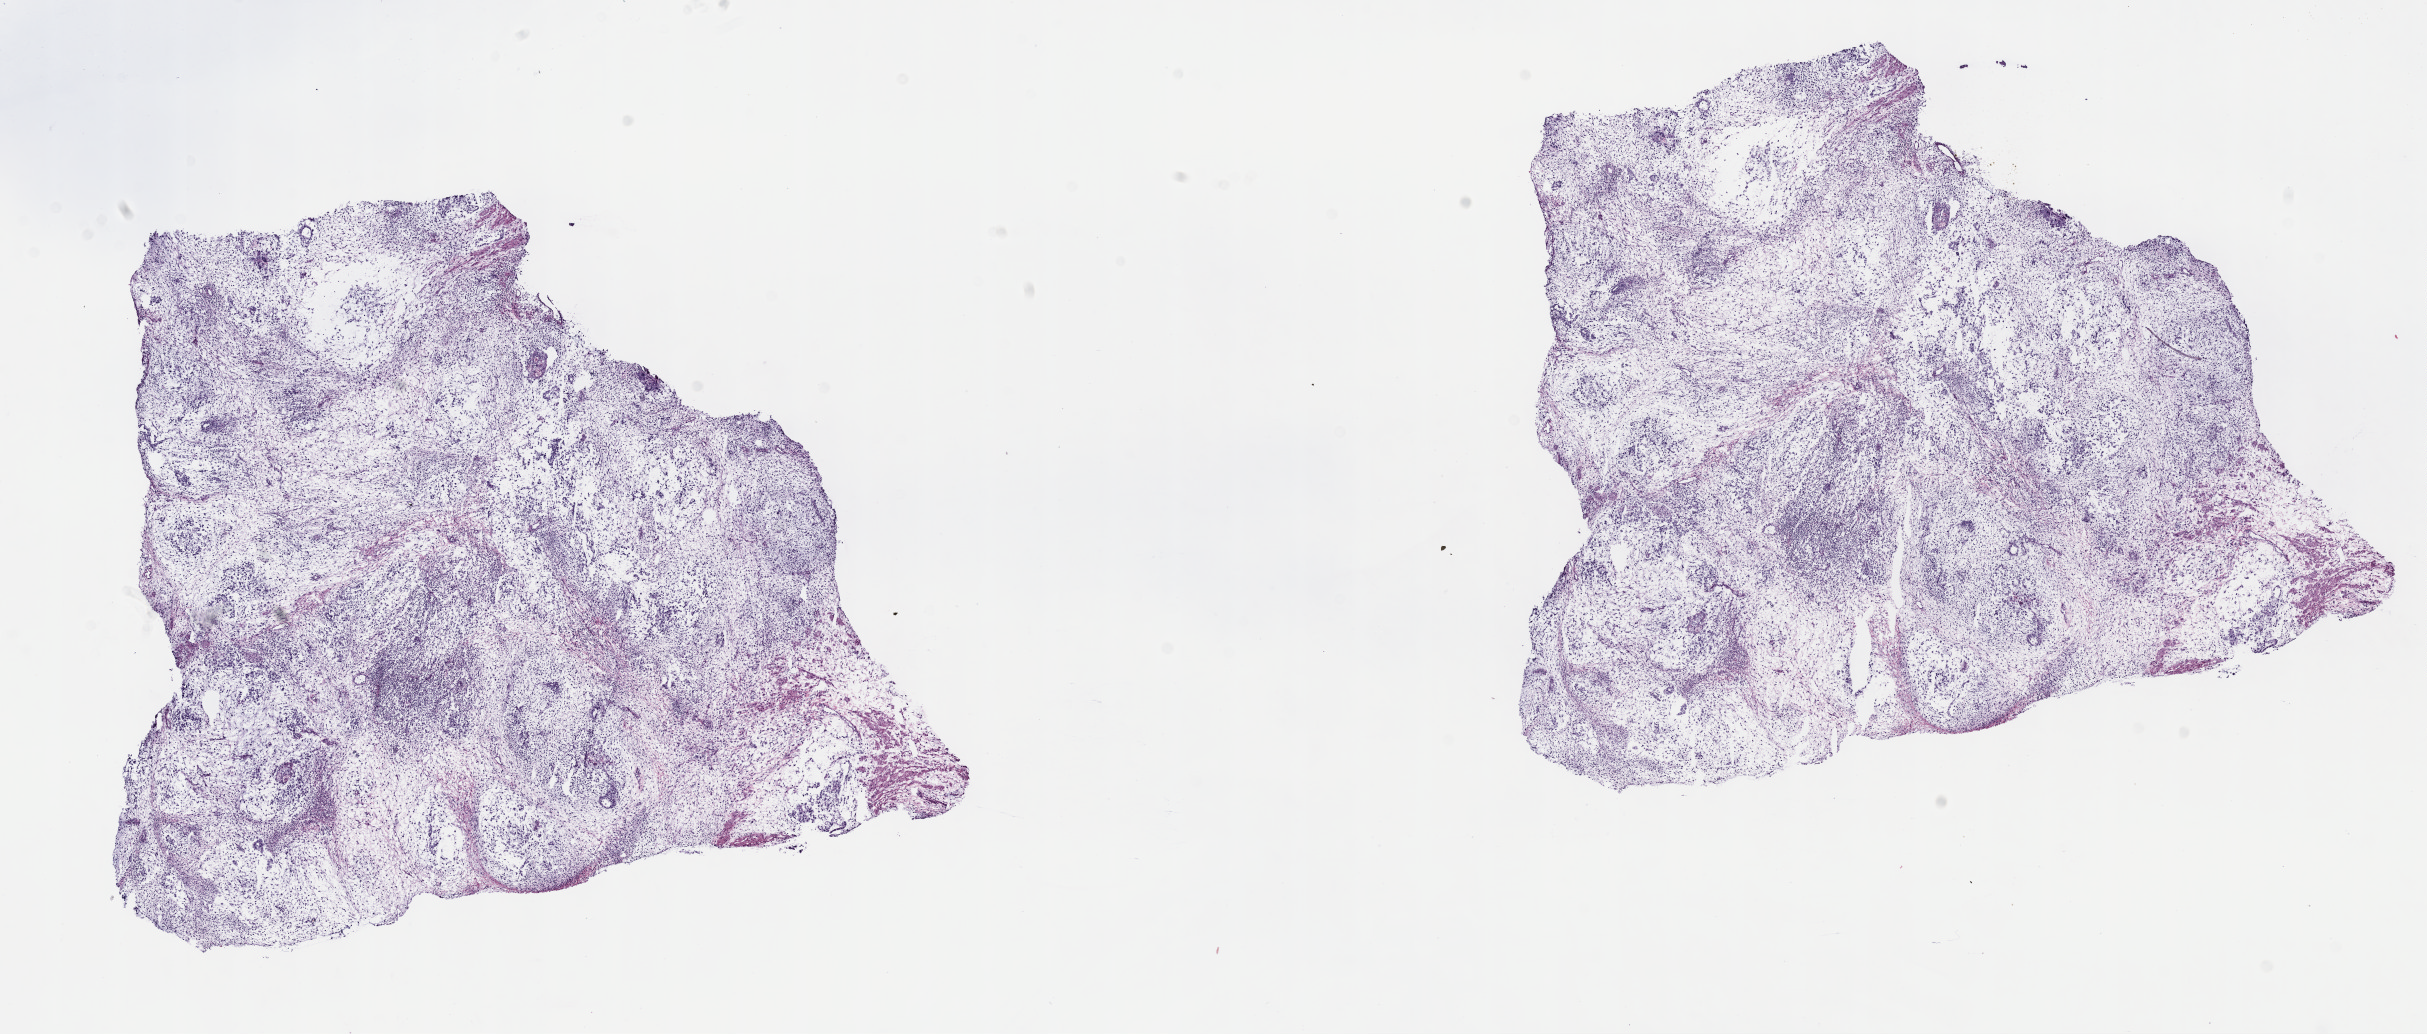
Digitized H&E tissue section (whole slide) — whole scanned area (about 19.6 x 8.4 mm, slide scanned at 40x) shown as a low-resolution overview, frozen section from the top of the tissue portion, primary tumour sample from the testis. Male, age 20 years at initial diagnosis. Composition of this section per pathologist review: tumour cells 100%, tumour nuclei 80%, normal cells 0%, stromal cells 0%, necrosis 0%. Infiltration values recorded for this section: lymphocyte infiltration 1%, monocyte infiltration 0%, neutrophil infiltration 0%.
• laterality: left
• diagnosis: Mixed germ cell tumor
• AJCC pathologic stage: IS (5th edition)